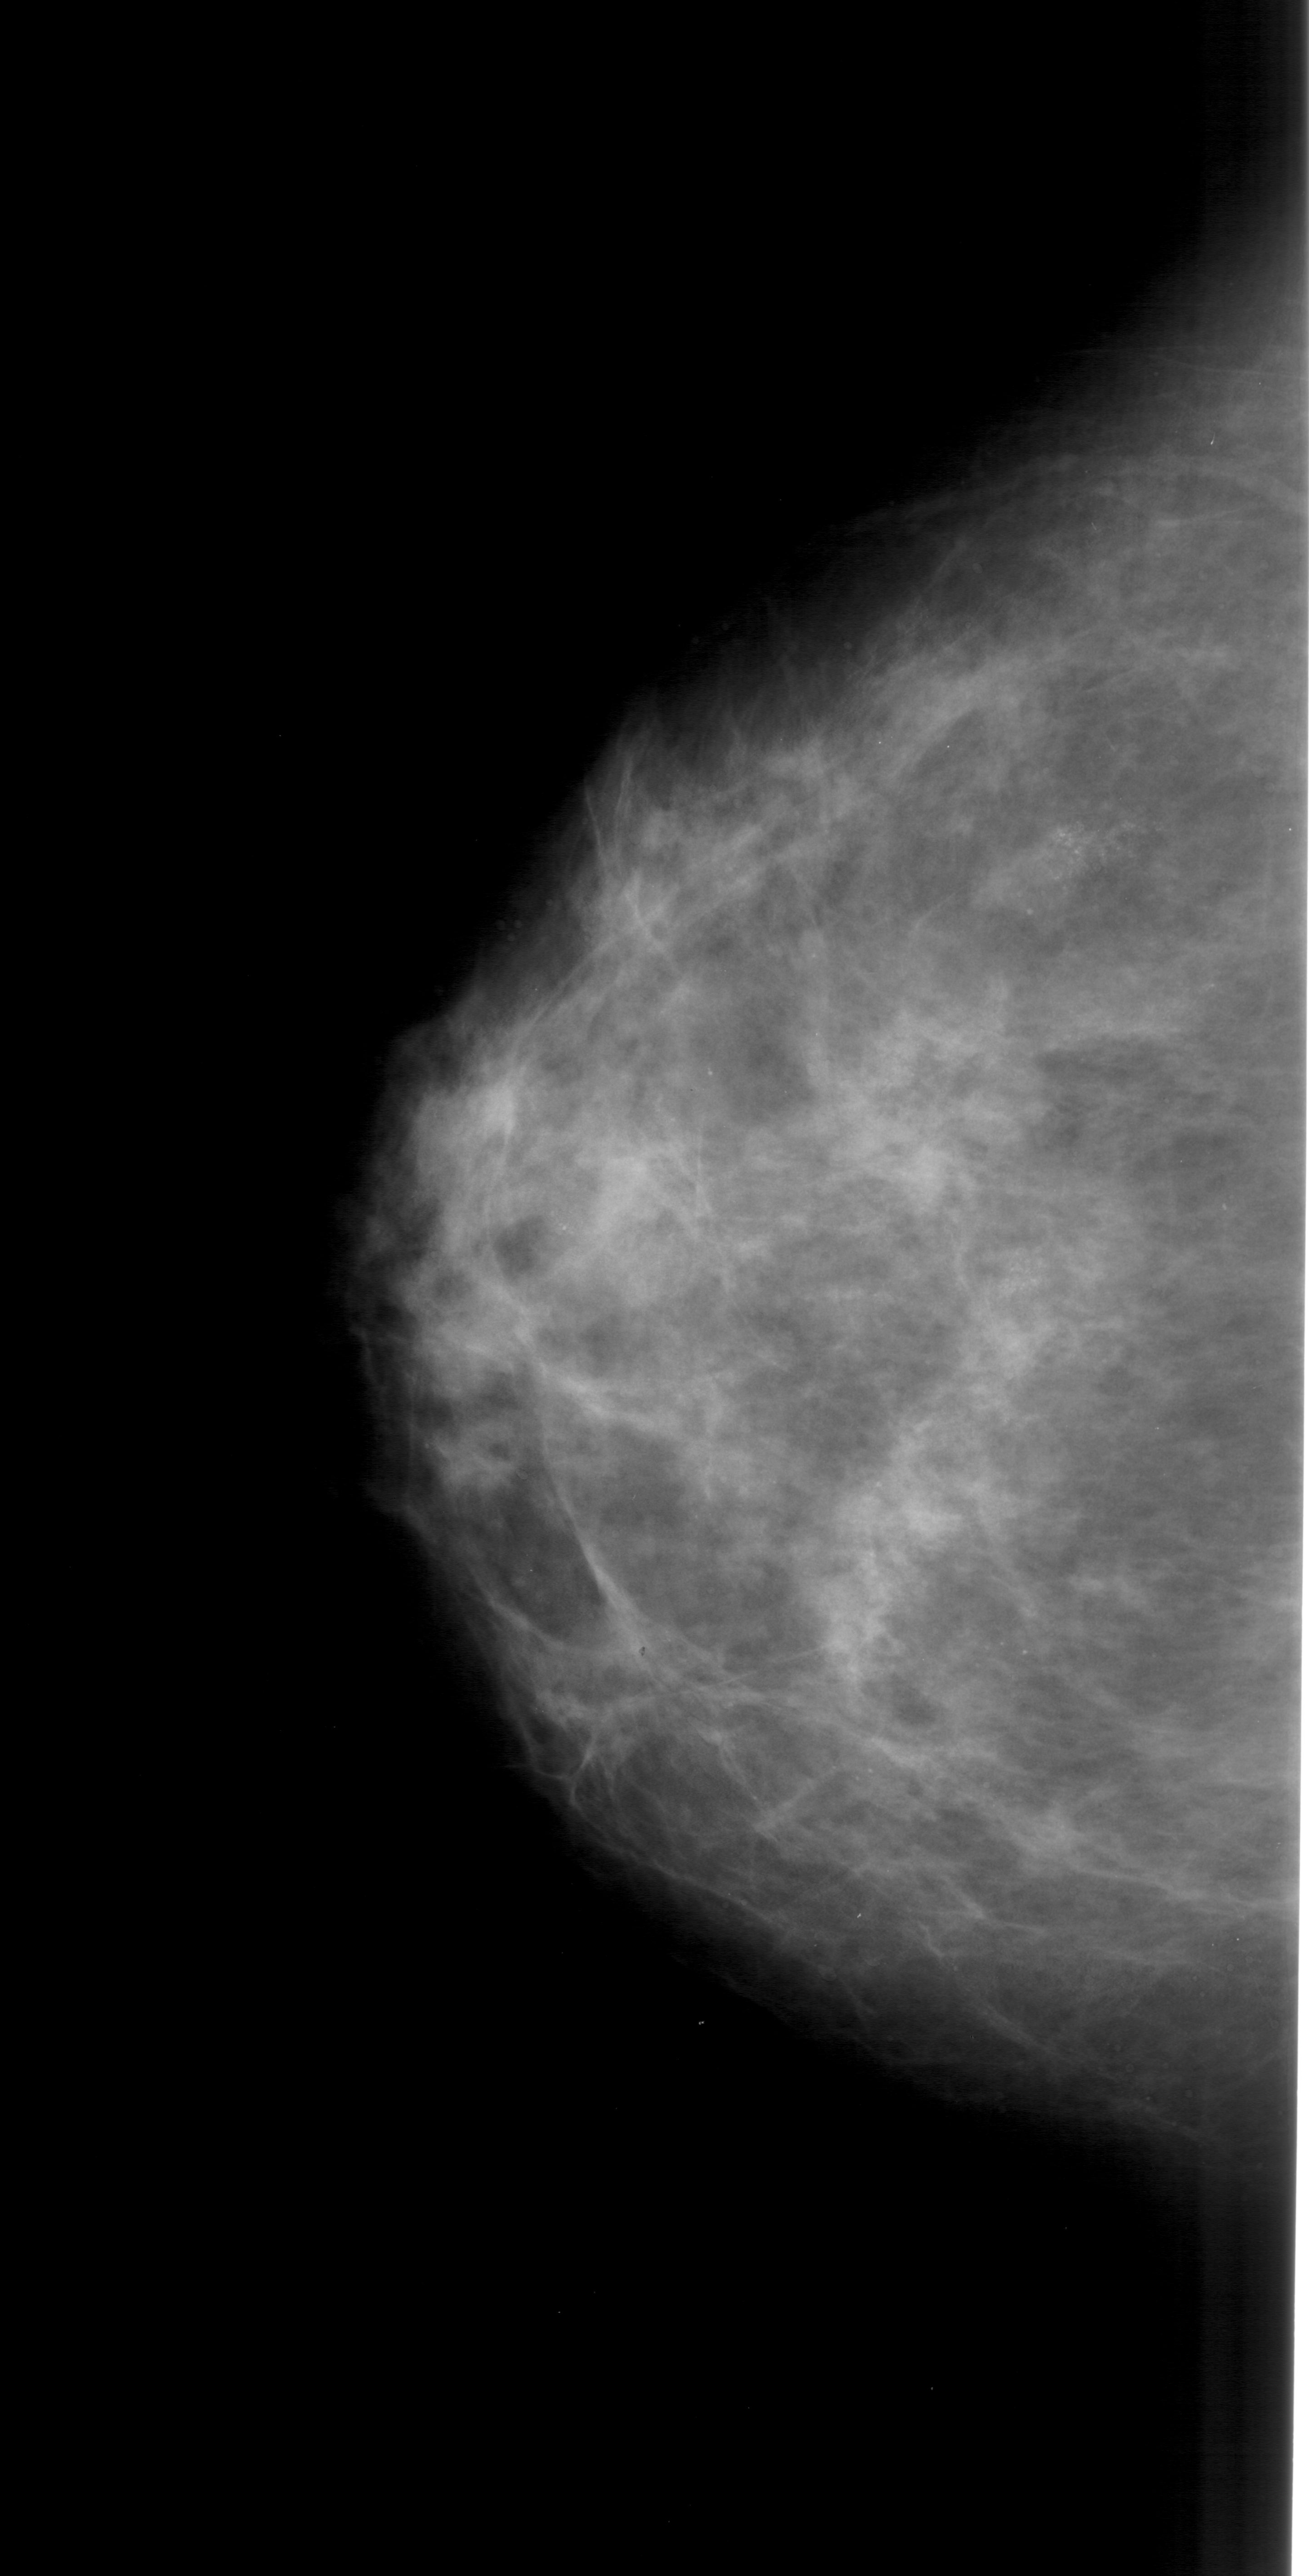
Mammogram (digitized film), left breast, craniocaudal (CC) view, BI-RADS breast density category 3 (scale 1–4).
- Finding: calcifications, morphology pleomorphic, distribution clustered; BI-RADS assessment category 4; subtlety rating 3 on a 1 (subtle) to 5 (obvious) scale; pathology (as recorded): malignant.